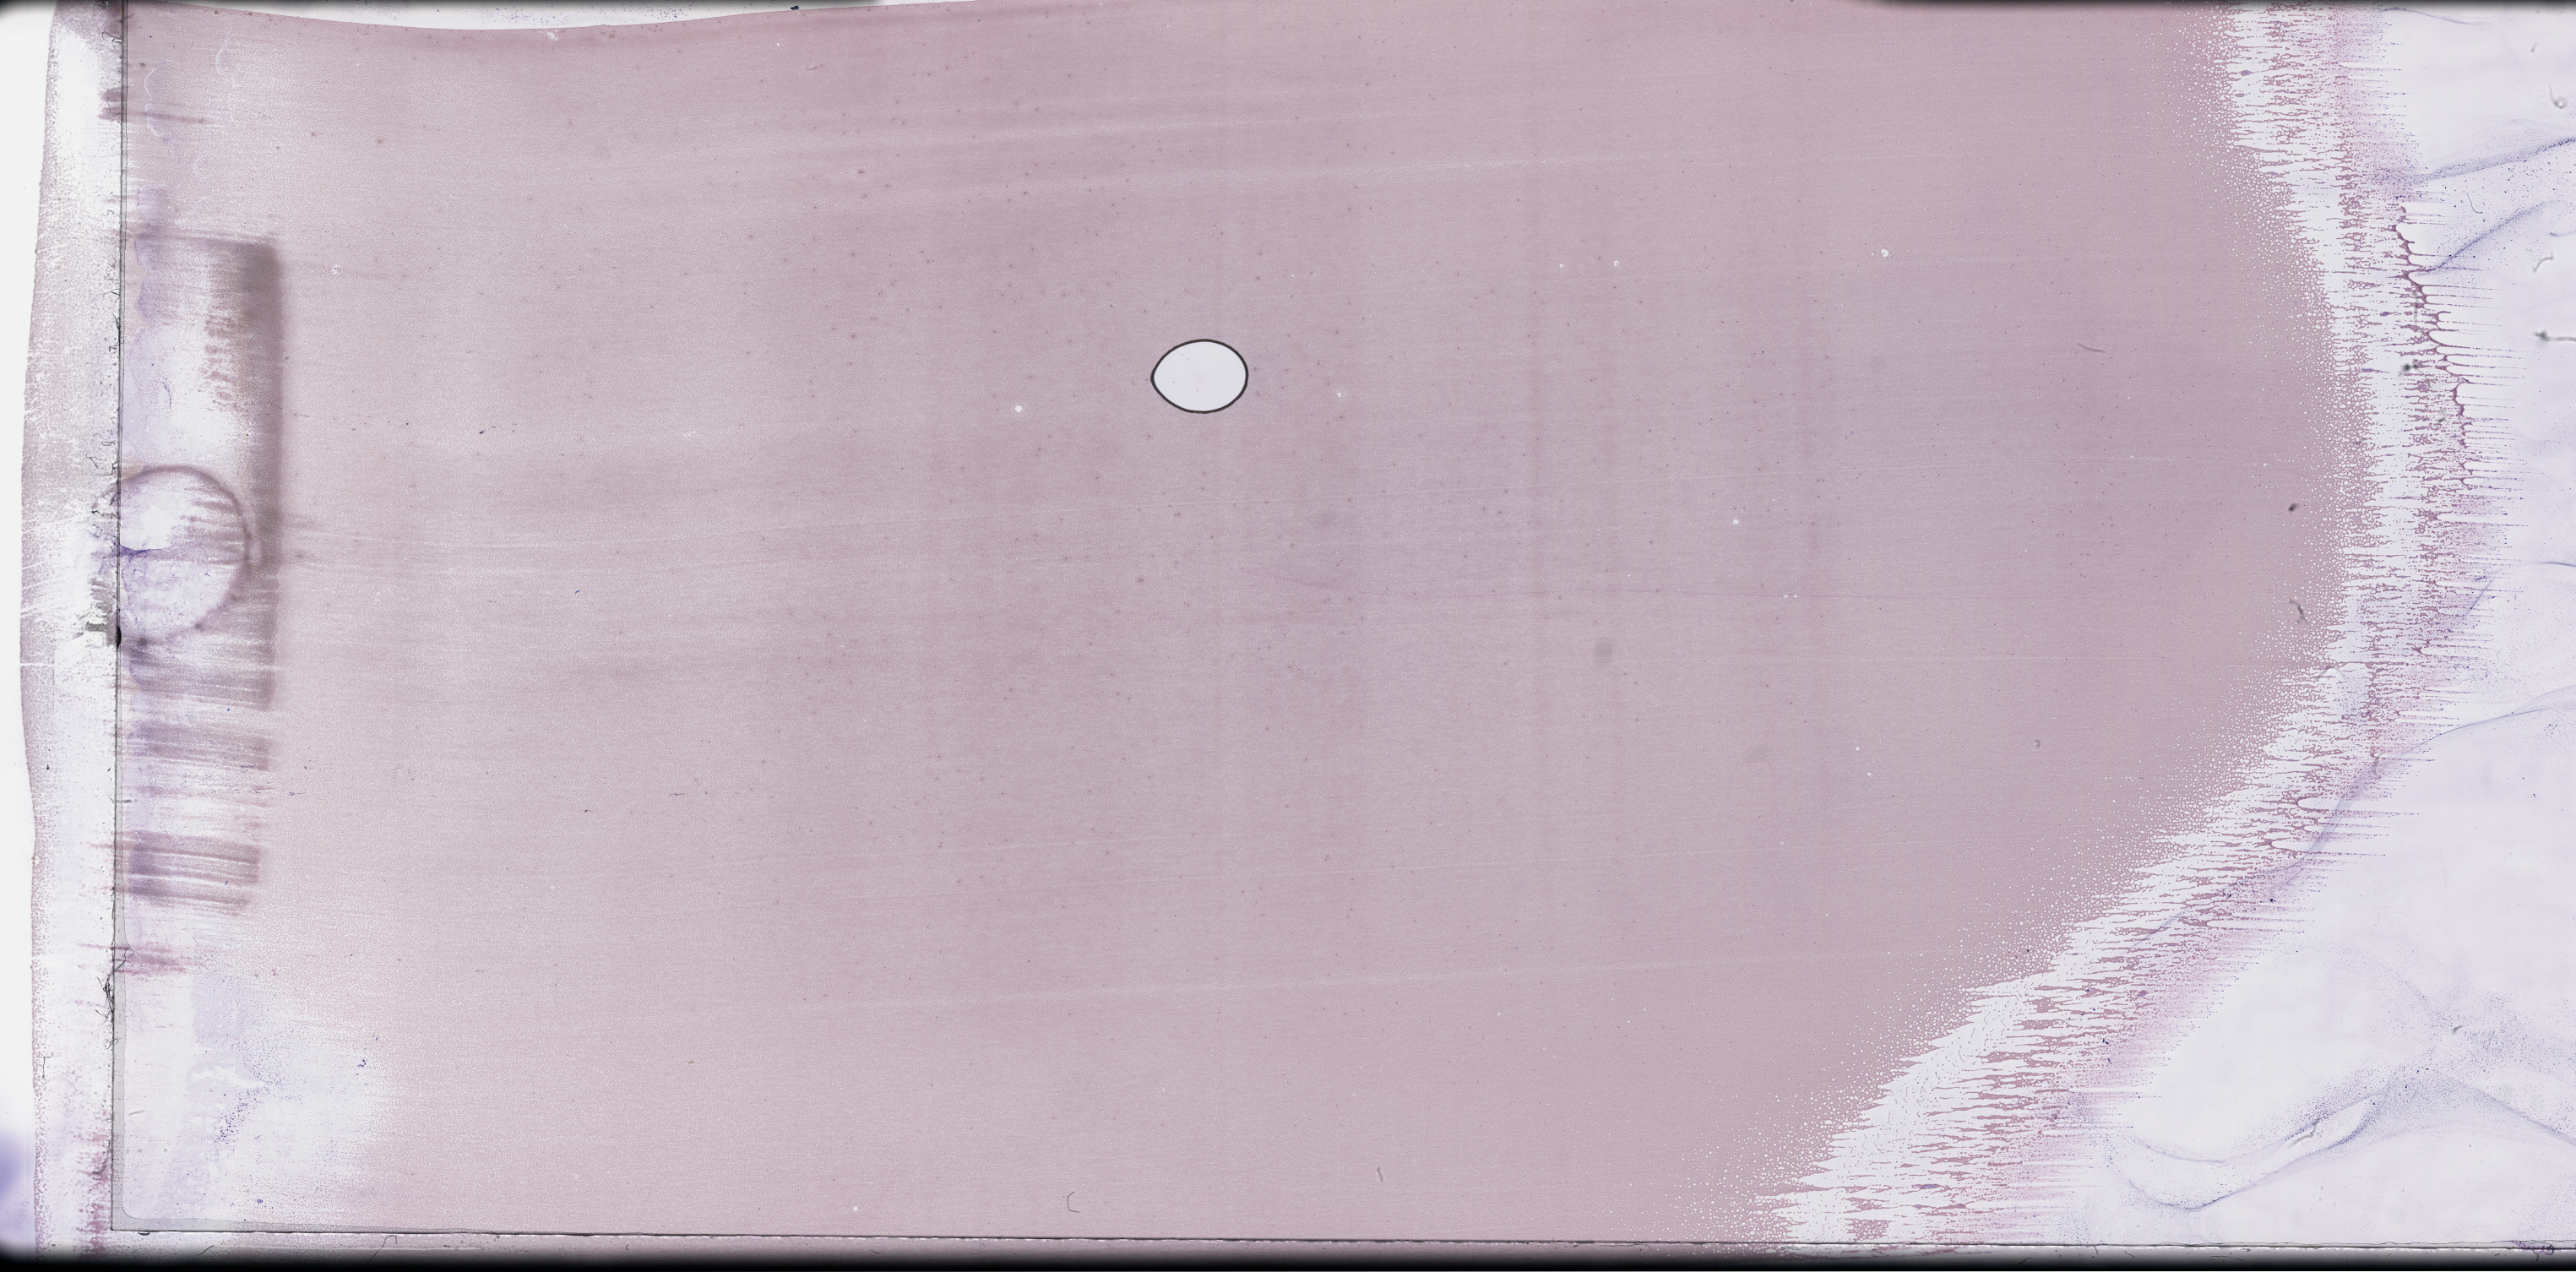
Wright-Giemsa-stained whole blood smear, whole-slide image — low-resolution overview of the scanned area, about 49.3 x 24.3 mm. Smear from an EDTA sample. Collected on treatment. Patient: male.
• from a patient with: Plasma Cell Myeloma